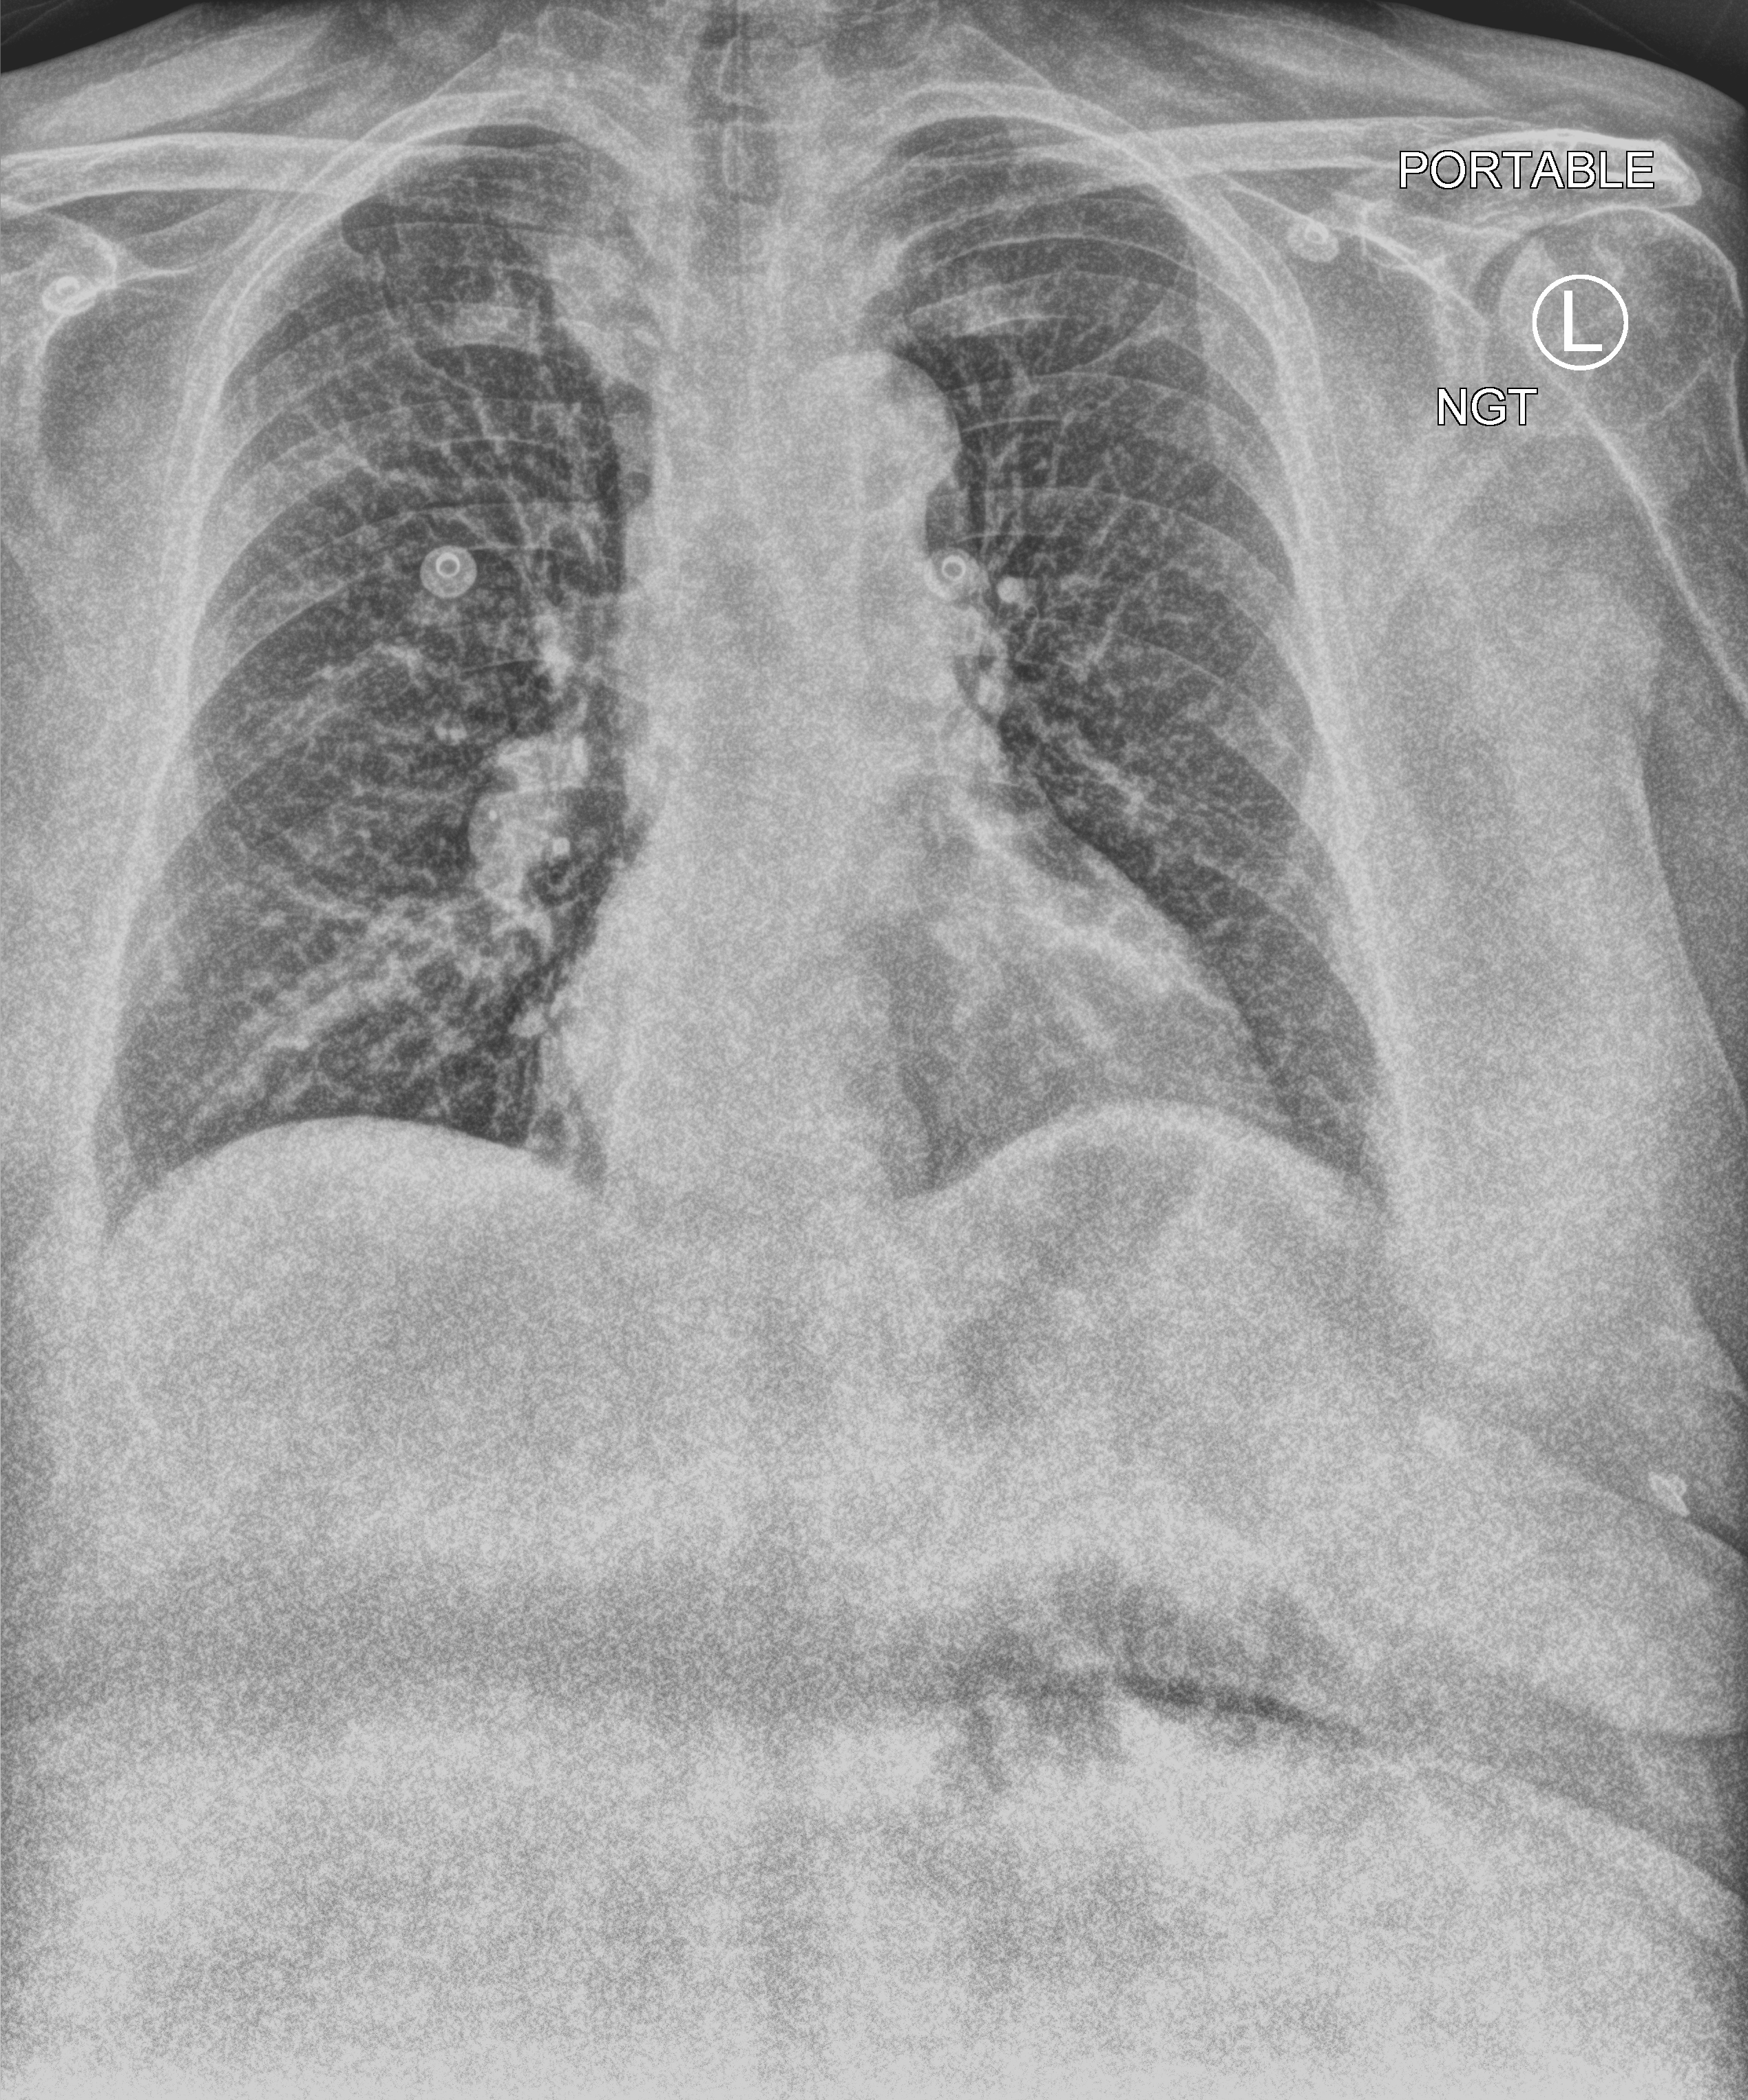
Bedside chest radiograph (computed radiography); anteroposterior (AP) projection. Patient hospitalised with COVID-19; female, aged 60–74 years.
Hospital-stay facts (about this admission, not read from this image; timing relative to this image not recorded): admitted to intensive care during this hospital stay: yes; mechanically ventilated during this hospital stay: no.